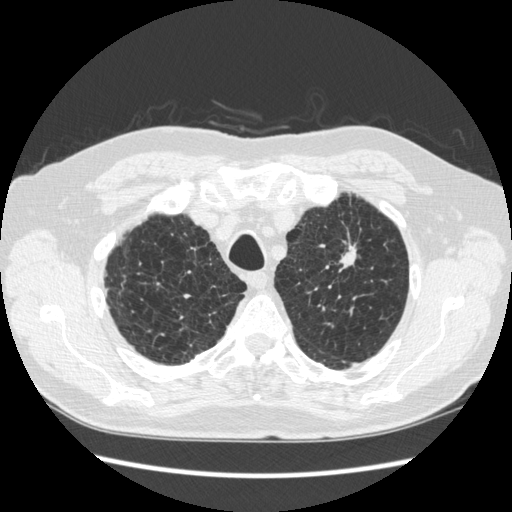
Axial slice from a low-dose chest CT screening exam, third annual screen, lung window (W 1500 / L -600 HU), 1.25 mm slice thickness, standard (soft-tissue) reconstruction kernel (STANDARD), 120 kVp, 512 × 512 image matrix. Male participant, aged 70 years at enrolment.
- Expert reader's lesion annotation, bounding box <323,218,374,283> (left, top, right, bottom; pixels).
- The screening reader recorded 2 non-calcified nodules or masses ≥4 mm on this exam; which of them this box marks is not recorded.
- Participant outcome: lung cancer diagnosed 92 days after this screen — squamous cell carcinoma, NOS, left upper lobe, moderately differentiated (G2), stage IA (AJCC 6th edition), 18 mm at pathology.